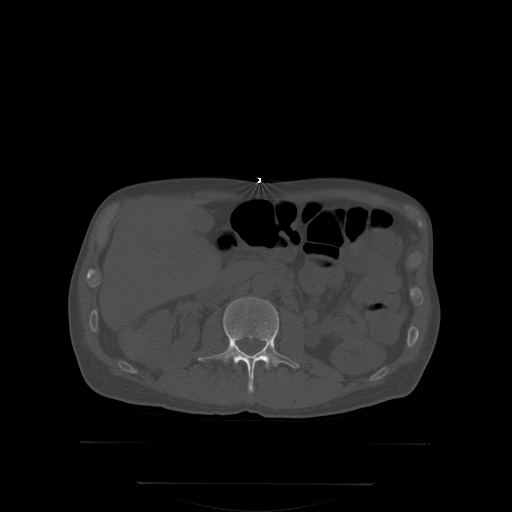
CT including the spine, one axial slice; position 138 of 350 along the scan axis; bone window (W 1800 / L 400 HU); 2.5 mm slice thickness; 512 × 512 image matrix. Male patient, age 58 years. Case-level facts recorded for this patient, not image findings: primary cancer: prostate; vertebrae with lytic lesions (as recorded): L1.
Annotated regions visible in this slice (semi-automatic segmentation, software-assisted and operator-edited):
- L2 vertebra: bounding box <197,297,300,393> (left, top, right, bottom; pixels)